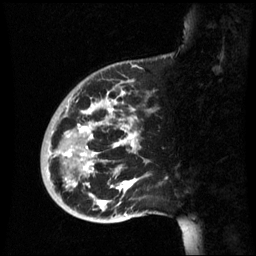
Breast MRI (dynamic contrast-enhanced), one sagittal slice. Position 17 of 60 along the scan axis. Dynamic contrast-enhanced series, image 2 of 3 at this slice position (ordered by acquisition). 1.5 T. TE 4.2 ms, TR 8.9 ms. 2.6 mm slice thickness. 256 × 256 image matrix. Female patient, age 35 years. Case-level facts recorded for this patient, not image findings: setting: breast cancer imaged before/during neoadjuvant chemotherapy; receptor status: HR-positive, HER2-negative.
Outlined on this slice (semi-automatically segmented with operator editing):
- analysis volume of interest (the breast-tissue region the enhancement analysis was run in; not a lesion): bounding box (x1, y1, x2, y2) in pixels: (40, 74, 162, 221)
- tumour enhancement mask (voxels above the 70 % enhancement threshold inside the analysis volume of interest): (63, 92, 138, 211)